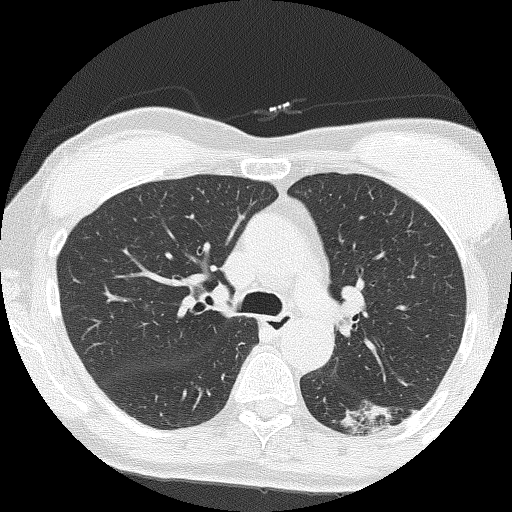
Chest CT (low-dose screening protocol), one axial image, second annual screen, lung window (W 1500 / L -600 HU), lung (sharp) reconstruction kernel (FC51), slice 55 of 159 in the series. Female, age 64 years at enrolment. Former smoker at enrolment.
Expert reader's lesion annotation, box from (x=354, y=390) to (x=417, y=439) px. The screening reader recorded 3 non-calcified nodules or masses ≥4 mm on this exam (right upper lobe, right upper lobe, right middle lobe); which of them this box marks is not recorded. Later outcome: lung cancer diagnosed 576 days after this screen (after the third annual screen) — adenocarcinoma, NOS, left lower lobe, moderately differentiated (G2), stage IA (AJCC 6th edition), 17 mm at pathology.